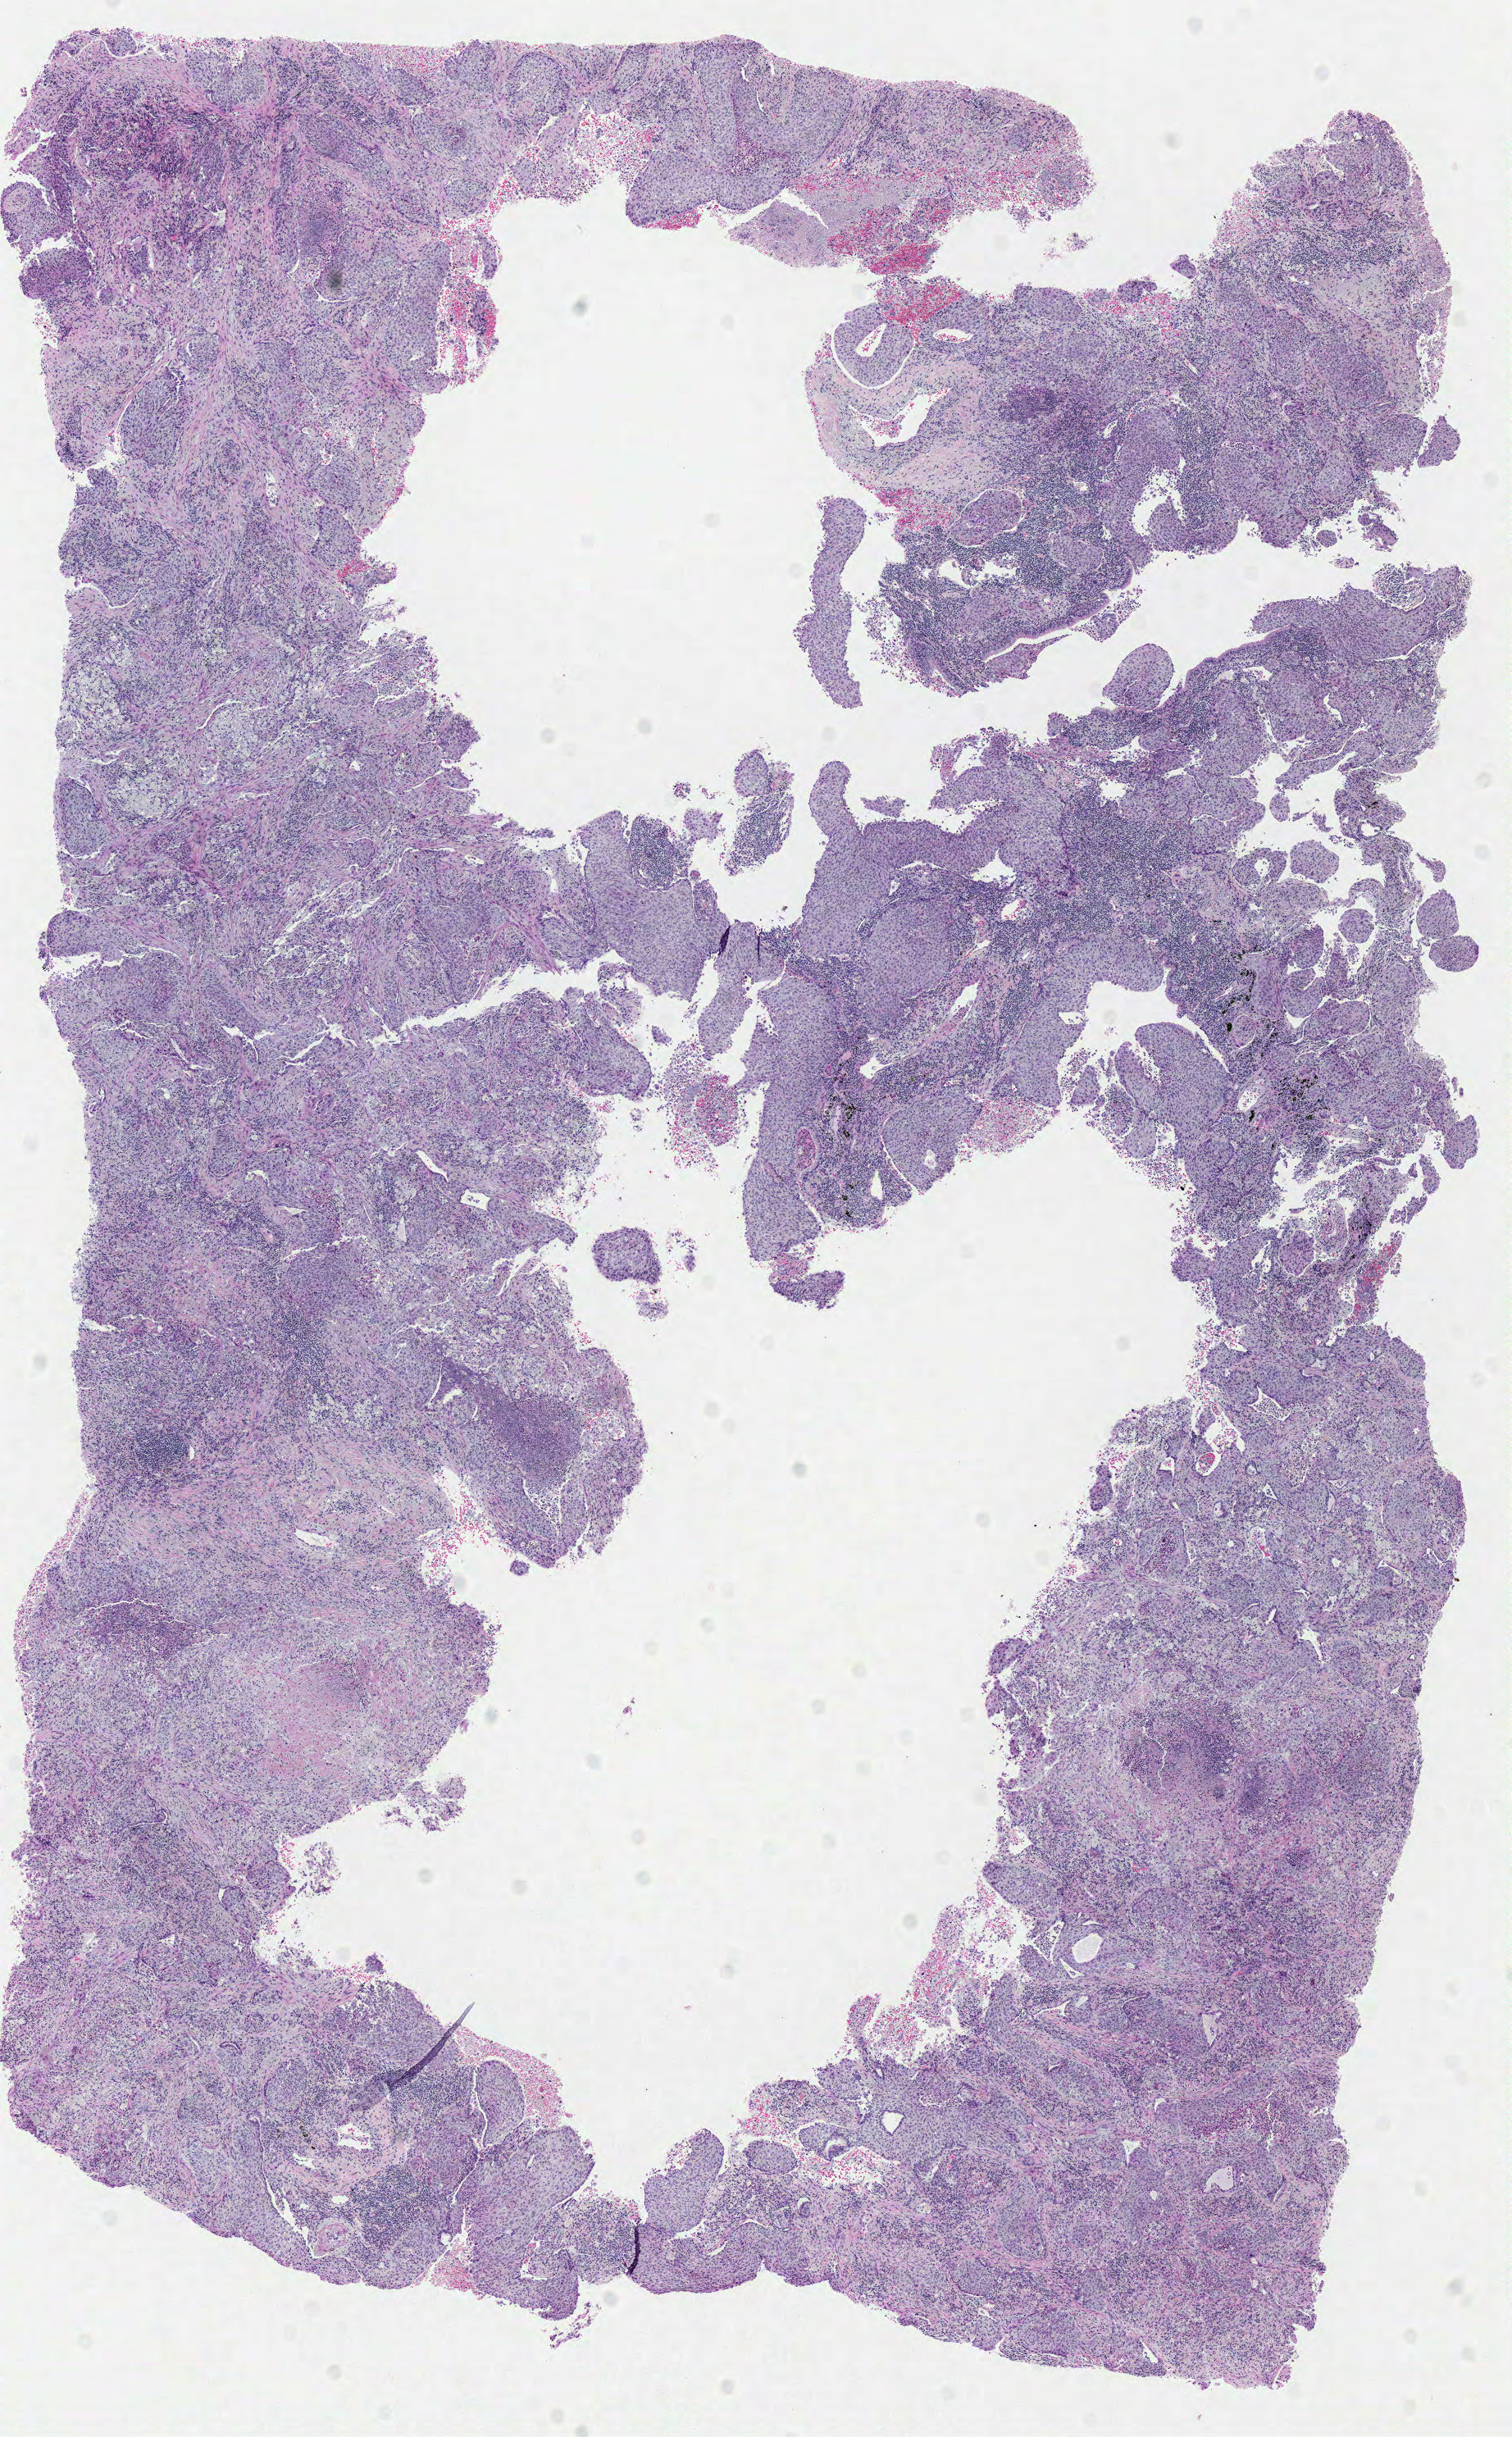
Whole-slide histology image, H&E — shown as a low-resolution overview of the whole scanned area (about 7.3 x 11.7 mm). Formalin-fixed paraffin-embedded (FFPE) diagnostic section. Lung, primary tumour sample. Patient: female, age at initial diagnosis 68 years.
AJCC pathologic stage: IIIB (6th edition). TNM: T2 N3 M0. Diagnosis: Squamous cell carcinoma, NOS (lower lobe, lung).